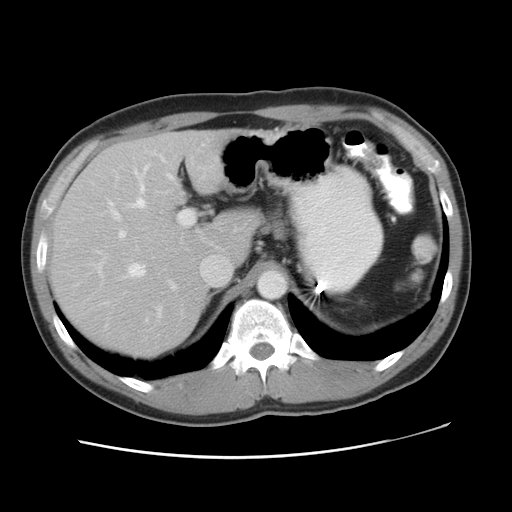
Contrast-enhanced abdominal CT, one axial slice; slice 33 of 49 in the series (ordered by position); reconstruction kernel STANDARD; 120 kVp; soft-tissue window (W 400 / L 40 HU); 512 × 512 image matrix, field of view 363 × 363 mm. Male patient, age 41 years. Case-level facts recorded for this patient, not image findings: diagnosis: colorectal cancer liver metastases, imaged before liver resection; multiple liver metastases: yes; largest metastasis: 0.7 cm.
Structures marked on this image (outlined manually by an expert reader):
- hepatic veins: box from (x=108, y=164) to (x=229, y=315) px
- liver: (x=48, y=131)–(x=252, y=359)
- planned liver remnant (the part of the liver to remain after resection): (x=101, y=131)–(x=253, y=264)
- portal vein (with intrahepatic branches): (x=98, y=210)–(x=194, y=320)